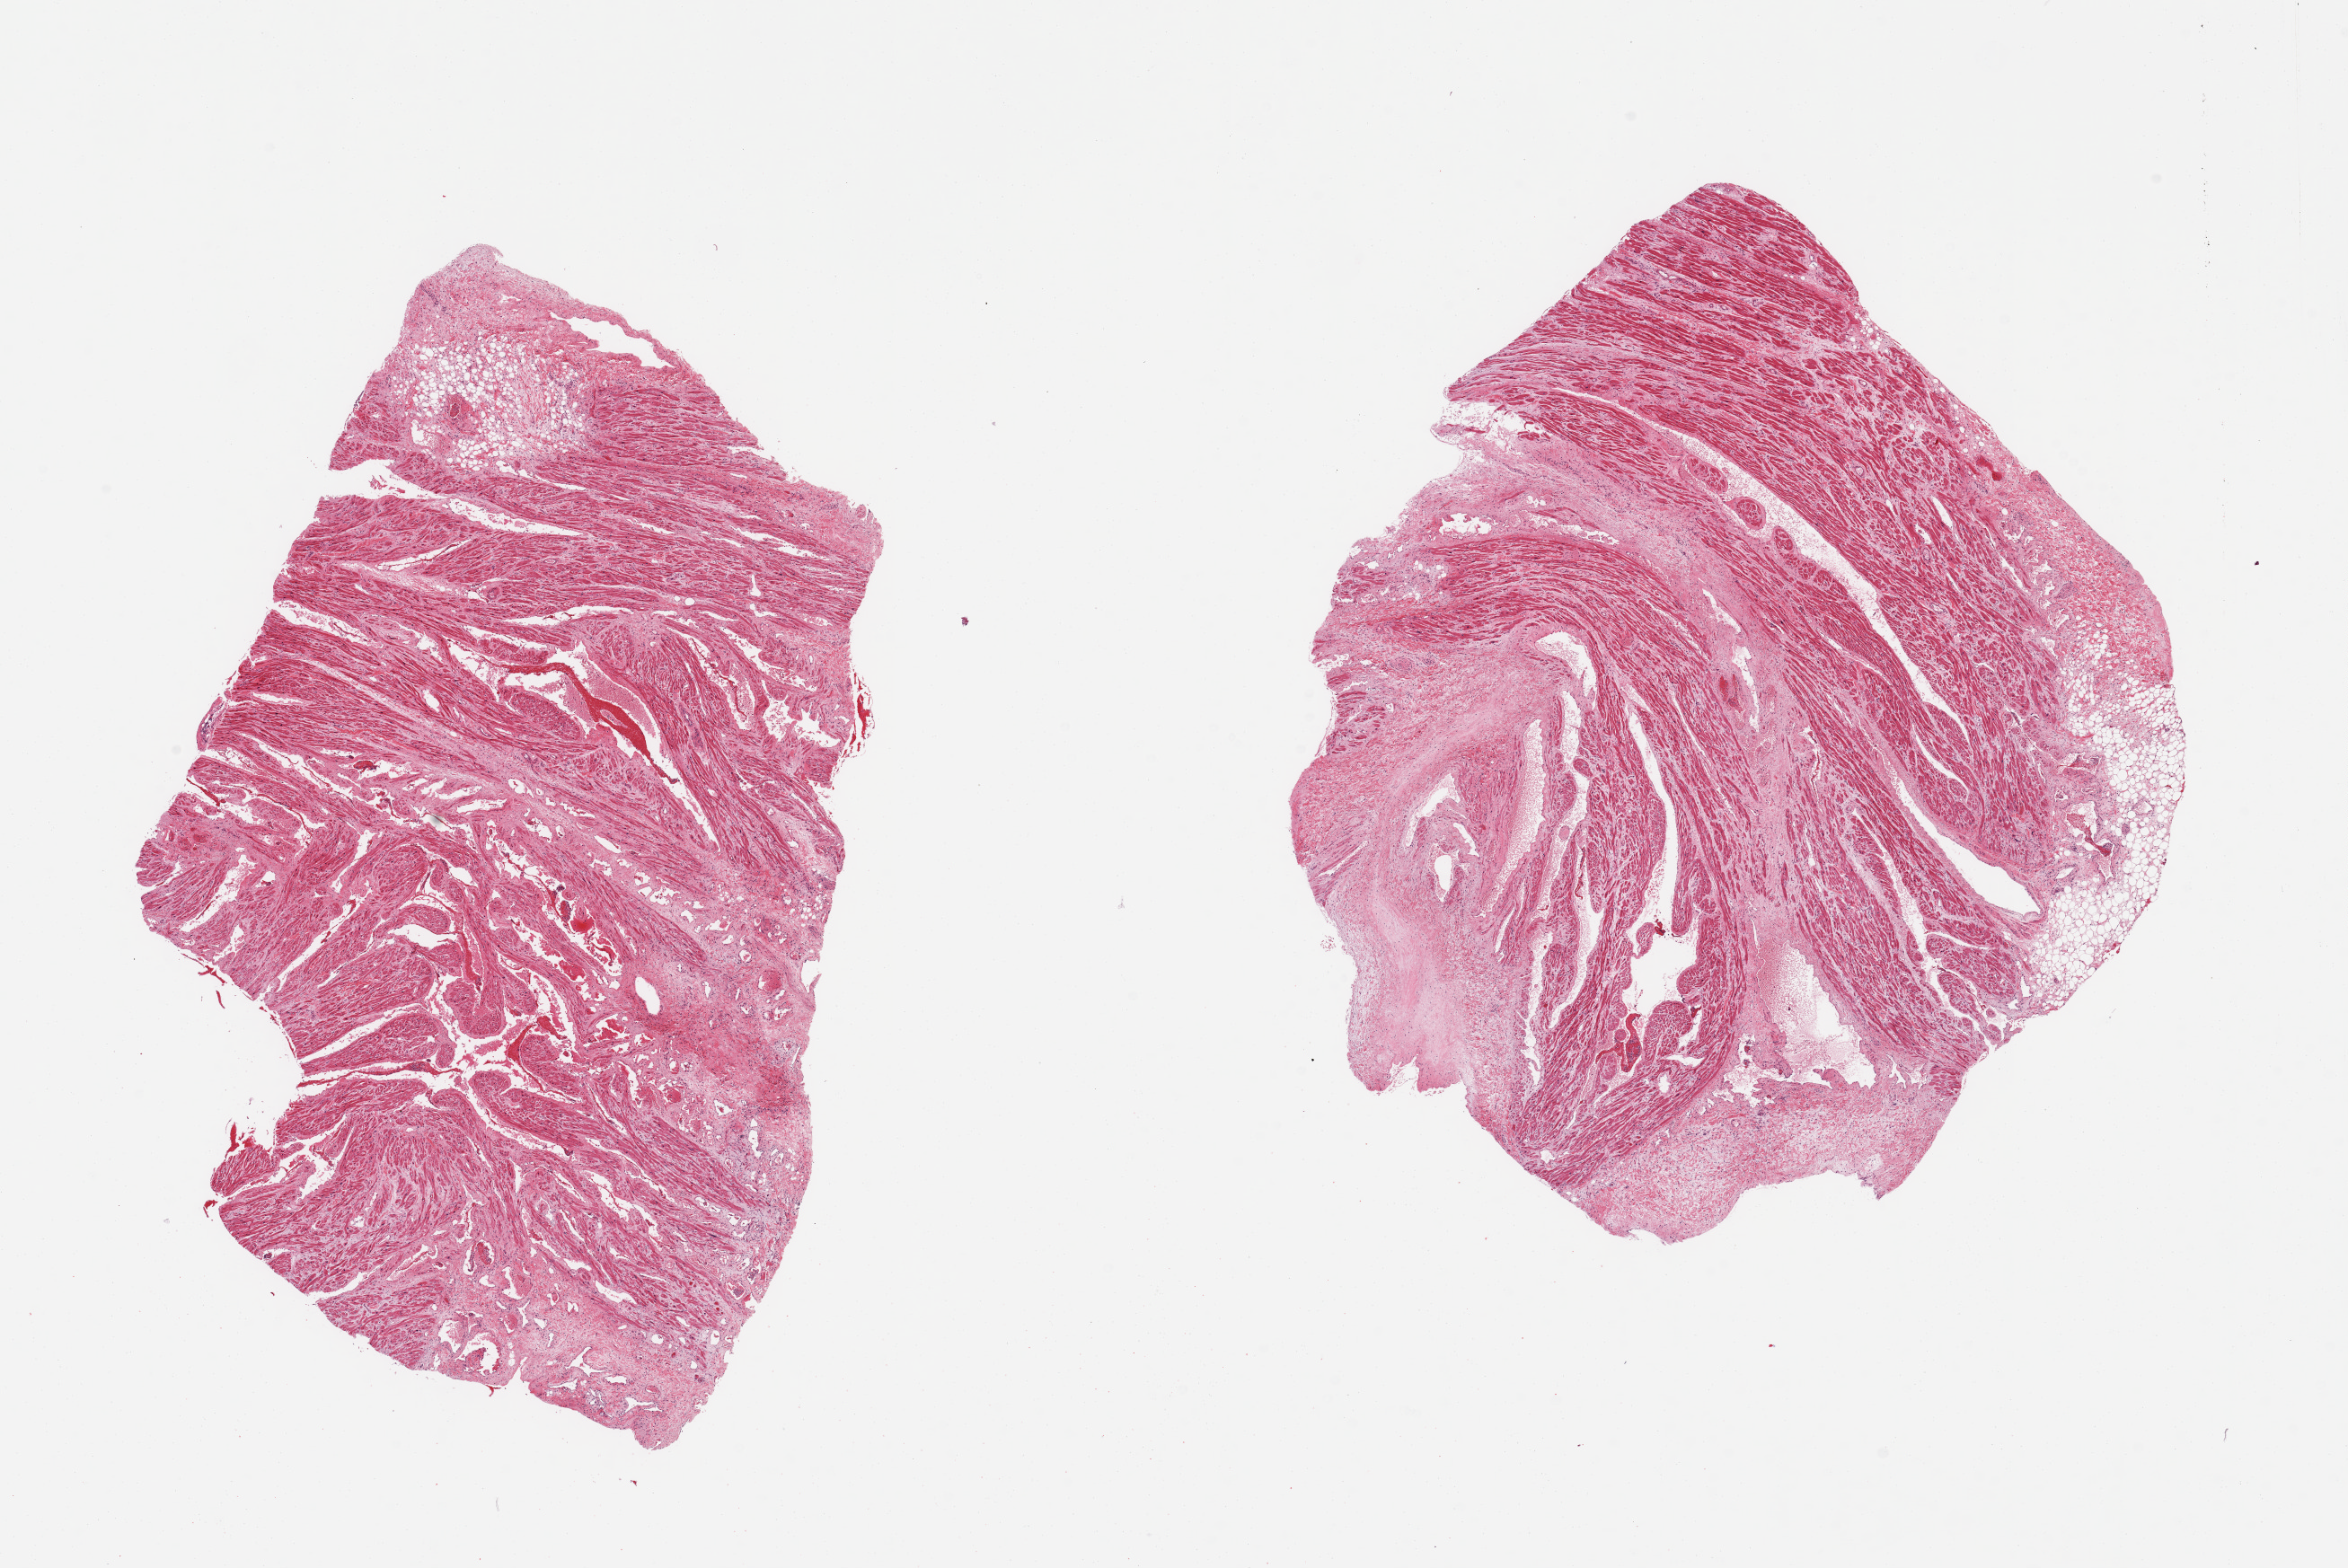
Hematoxylin and eosin (H&E) whole-slide image, whole scanned area (about 20.7 x 13.8 mm, acquisition: 20x scan) shown as a low-resolution overview. PAXgene-fixed paraffin-embedded (PFPE) section. Sampled site (target tissue): auricular appendage. Tissue donor sample. Donor sex: female.
• review note (as recorded): 2 pieces; 30% fibrofatty content